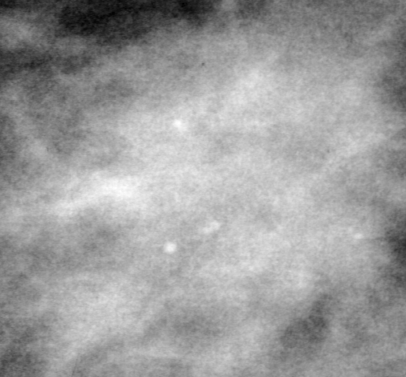
Crop from a digitized film mammogram around one marked abnormality, left breast, MLO view, BI-RADS breast density category 3 (scale 1–4).
Marked abnormality: mass, shape irregular, margins spiculated; BI-RADS assessment category 5; subtlety rating 3 on a 1 (subtle) to 5 (obvious) scale; pathology result (as recorded, not read from the image): malignant.